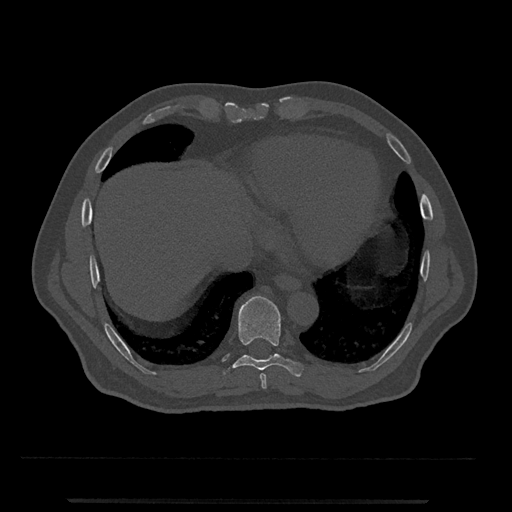
CT including the spine, one axial slice. Slice 572 of 797 in the series (ordered by position). 120 kVp. Bone window (W 1800 / L 400 HU). 0.5 mm slice thickness. 512 × 512 image matrix, field of view 419 × 419 mm. Male patient, age 63 years. Case-level facts recorded for this patient, not image findings: primary cancer: prostate.
Outlined on this slice (semi-automatic segmentation, software-assisted and operator-edited):
- T8 vertebra: bounding box (x1, y1, x2, y2) in pixels: (259, 373, 267, 389)
- T9 vertebra: (223, 296, 304, 377)